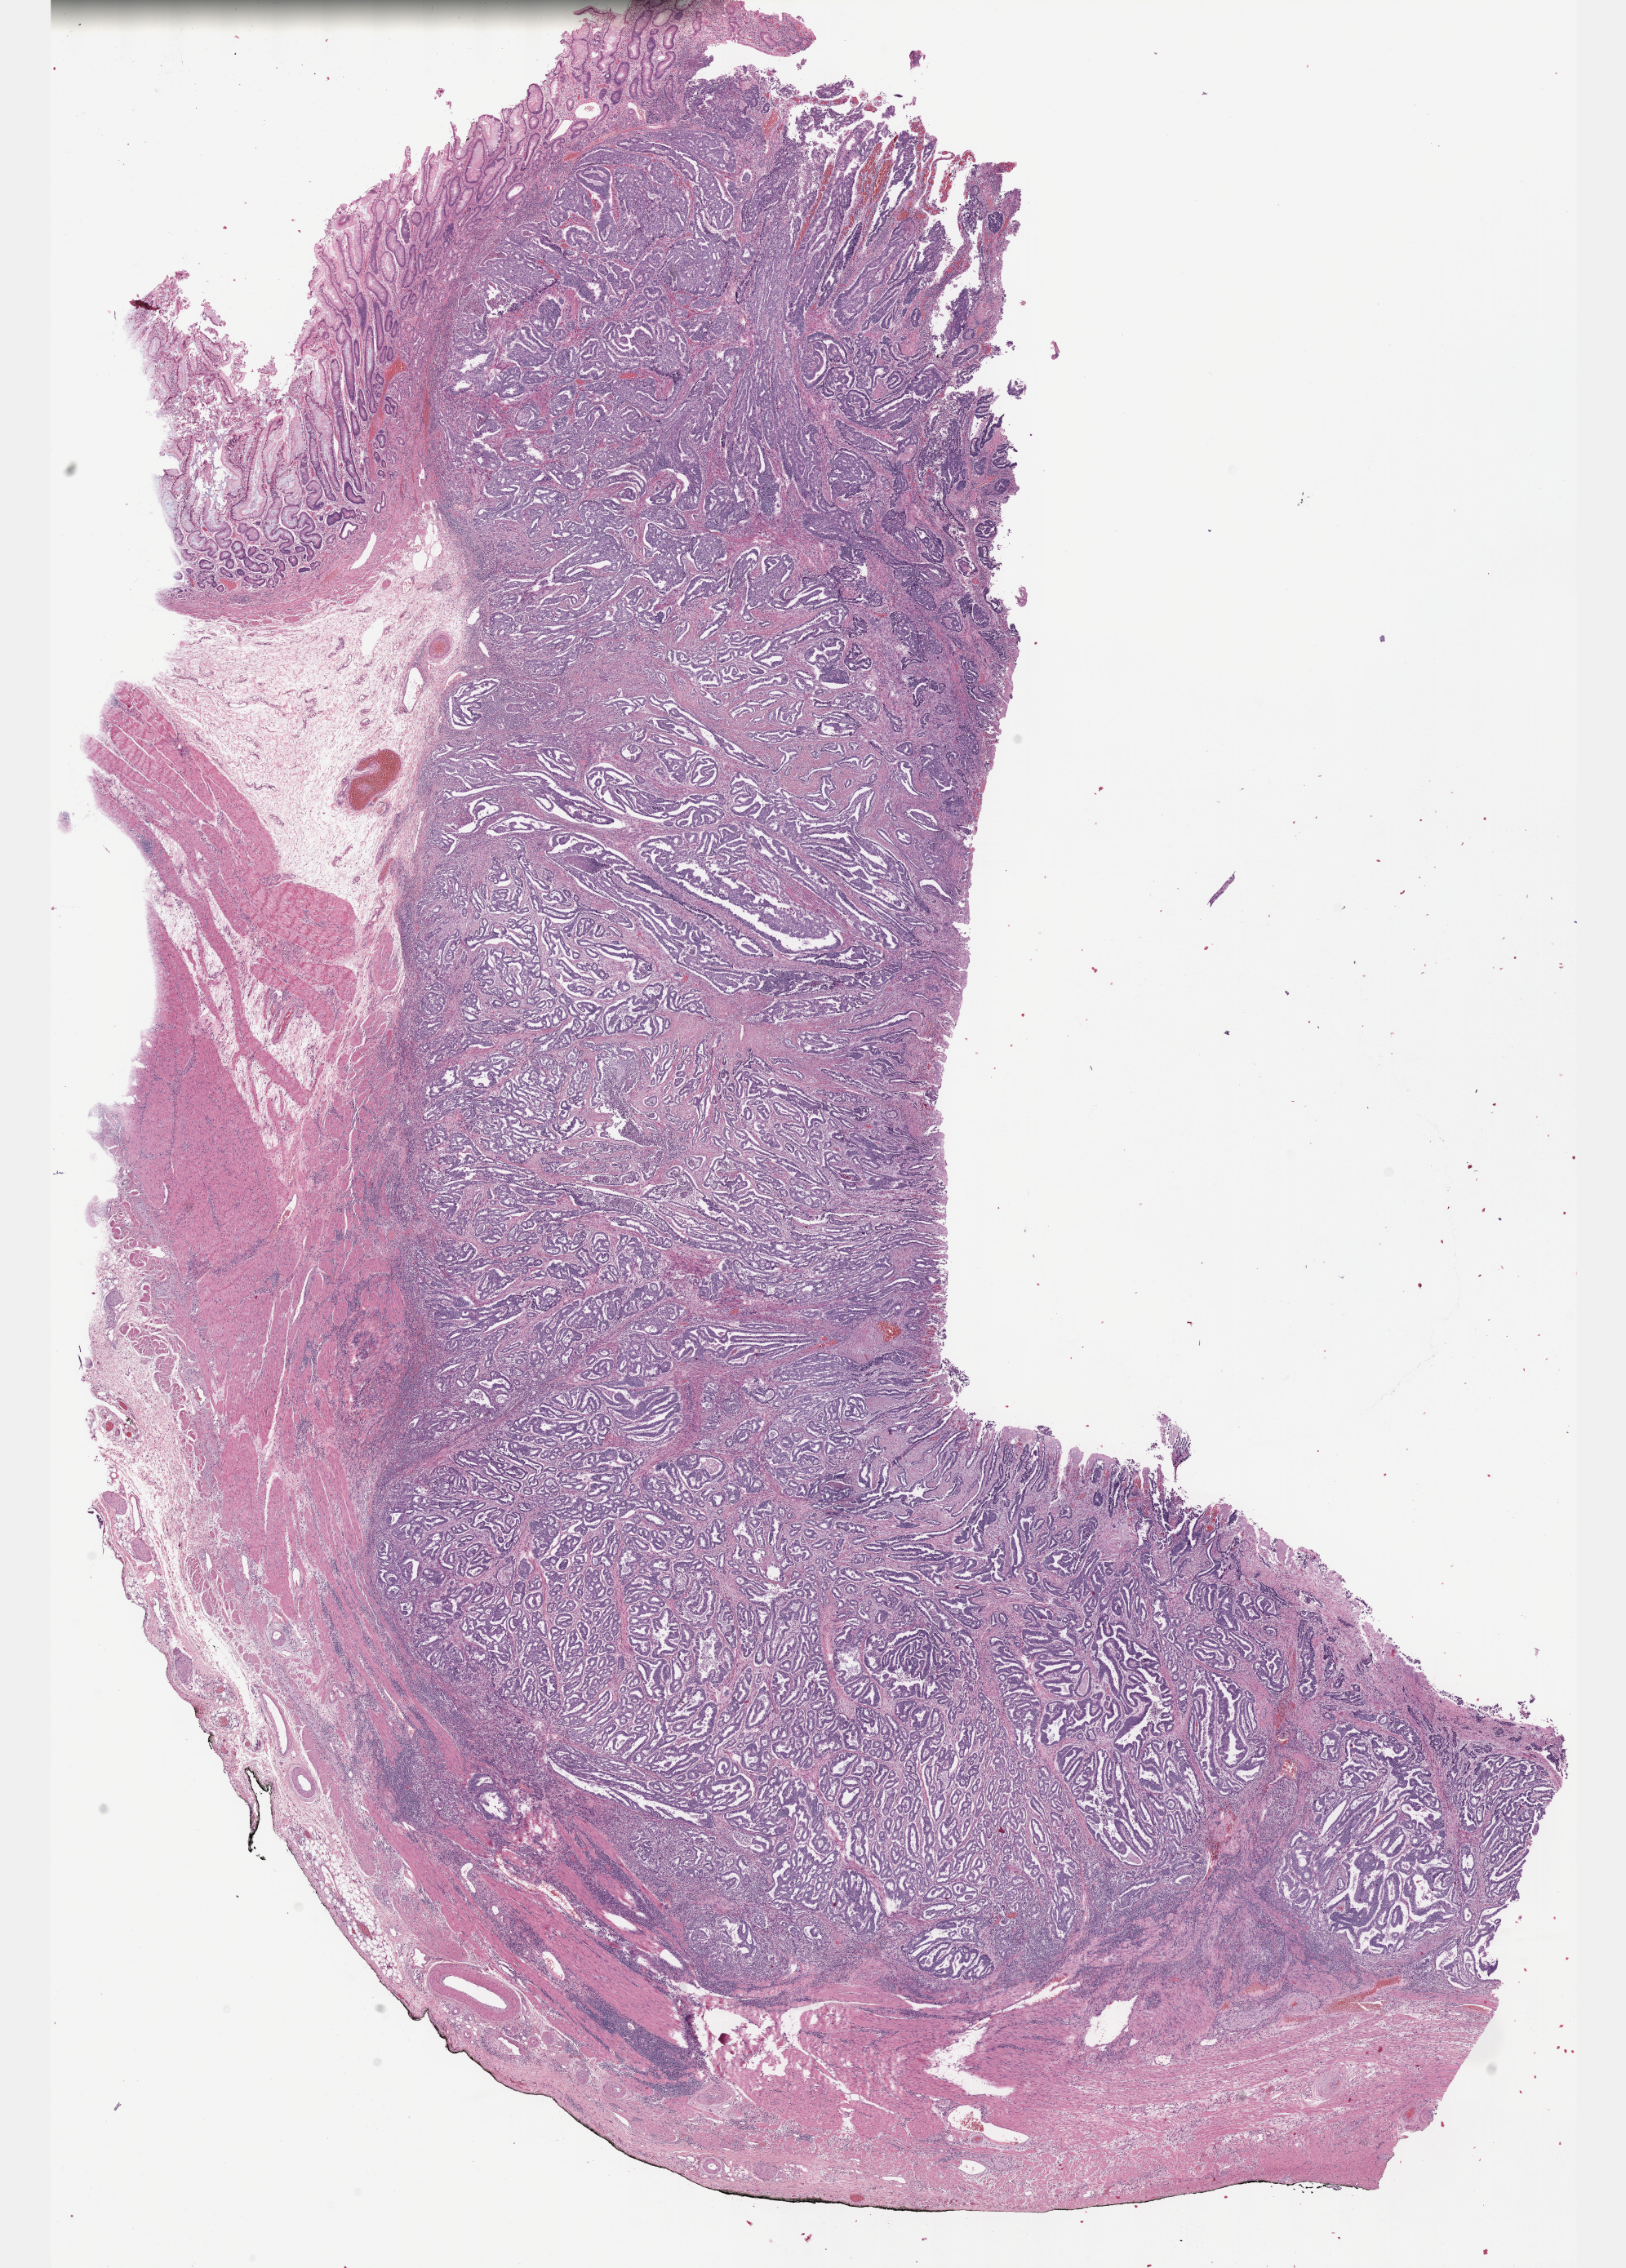
H&E whole-slide image, a low-resolution overview of the entire scanned area, about 16.1 x 22.5 mm (from a 40x scan); formalin-fixed paraffin-embedded (FFPE) diagnostic section; primary tumour sample from the stomach. Male, age 63 years at initial diagnosis. Histologic grade: G2 (moderately differentiated).
Diagnosis: Tubular adenocarcinoma (gastric antrum). AJCC pathologic stage: IIIA. Lymph nodes positive (case pathology): 8 of 23 examined.